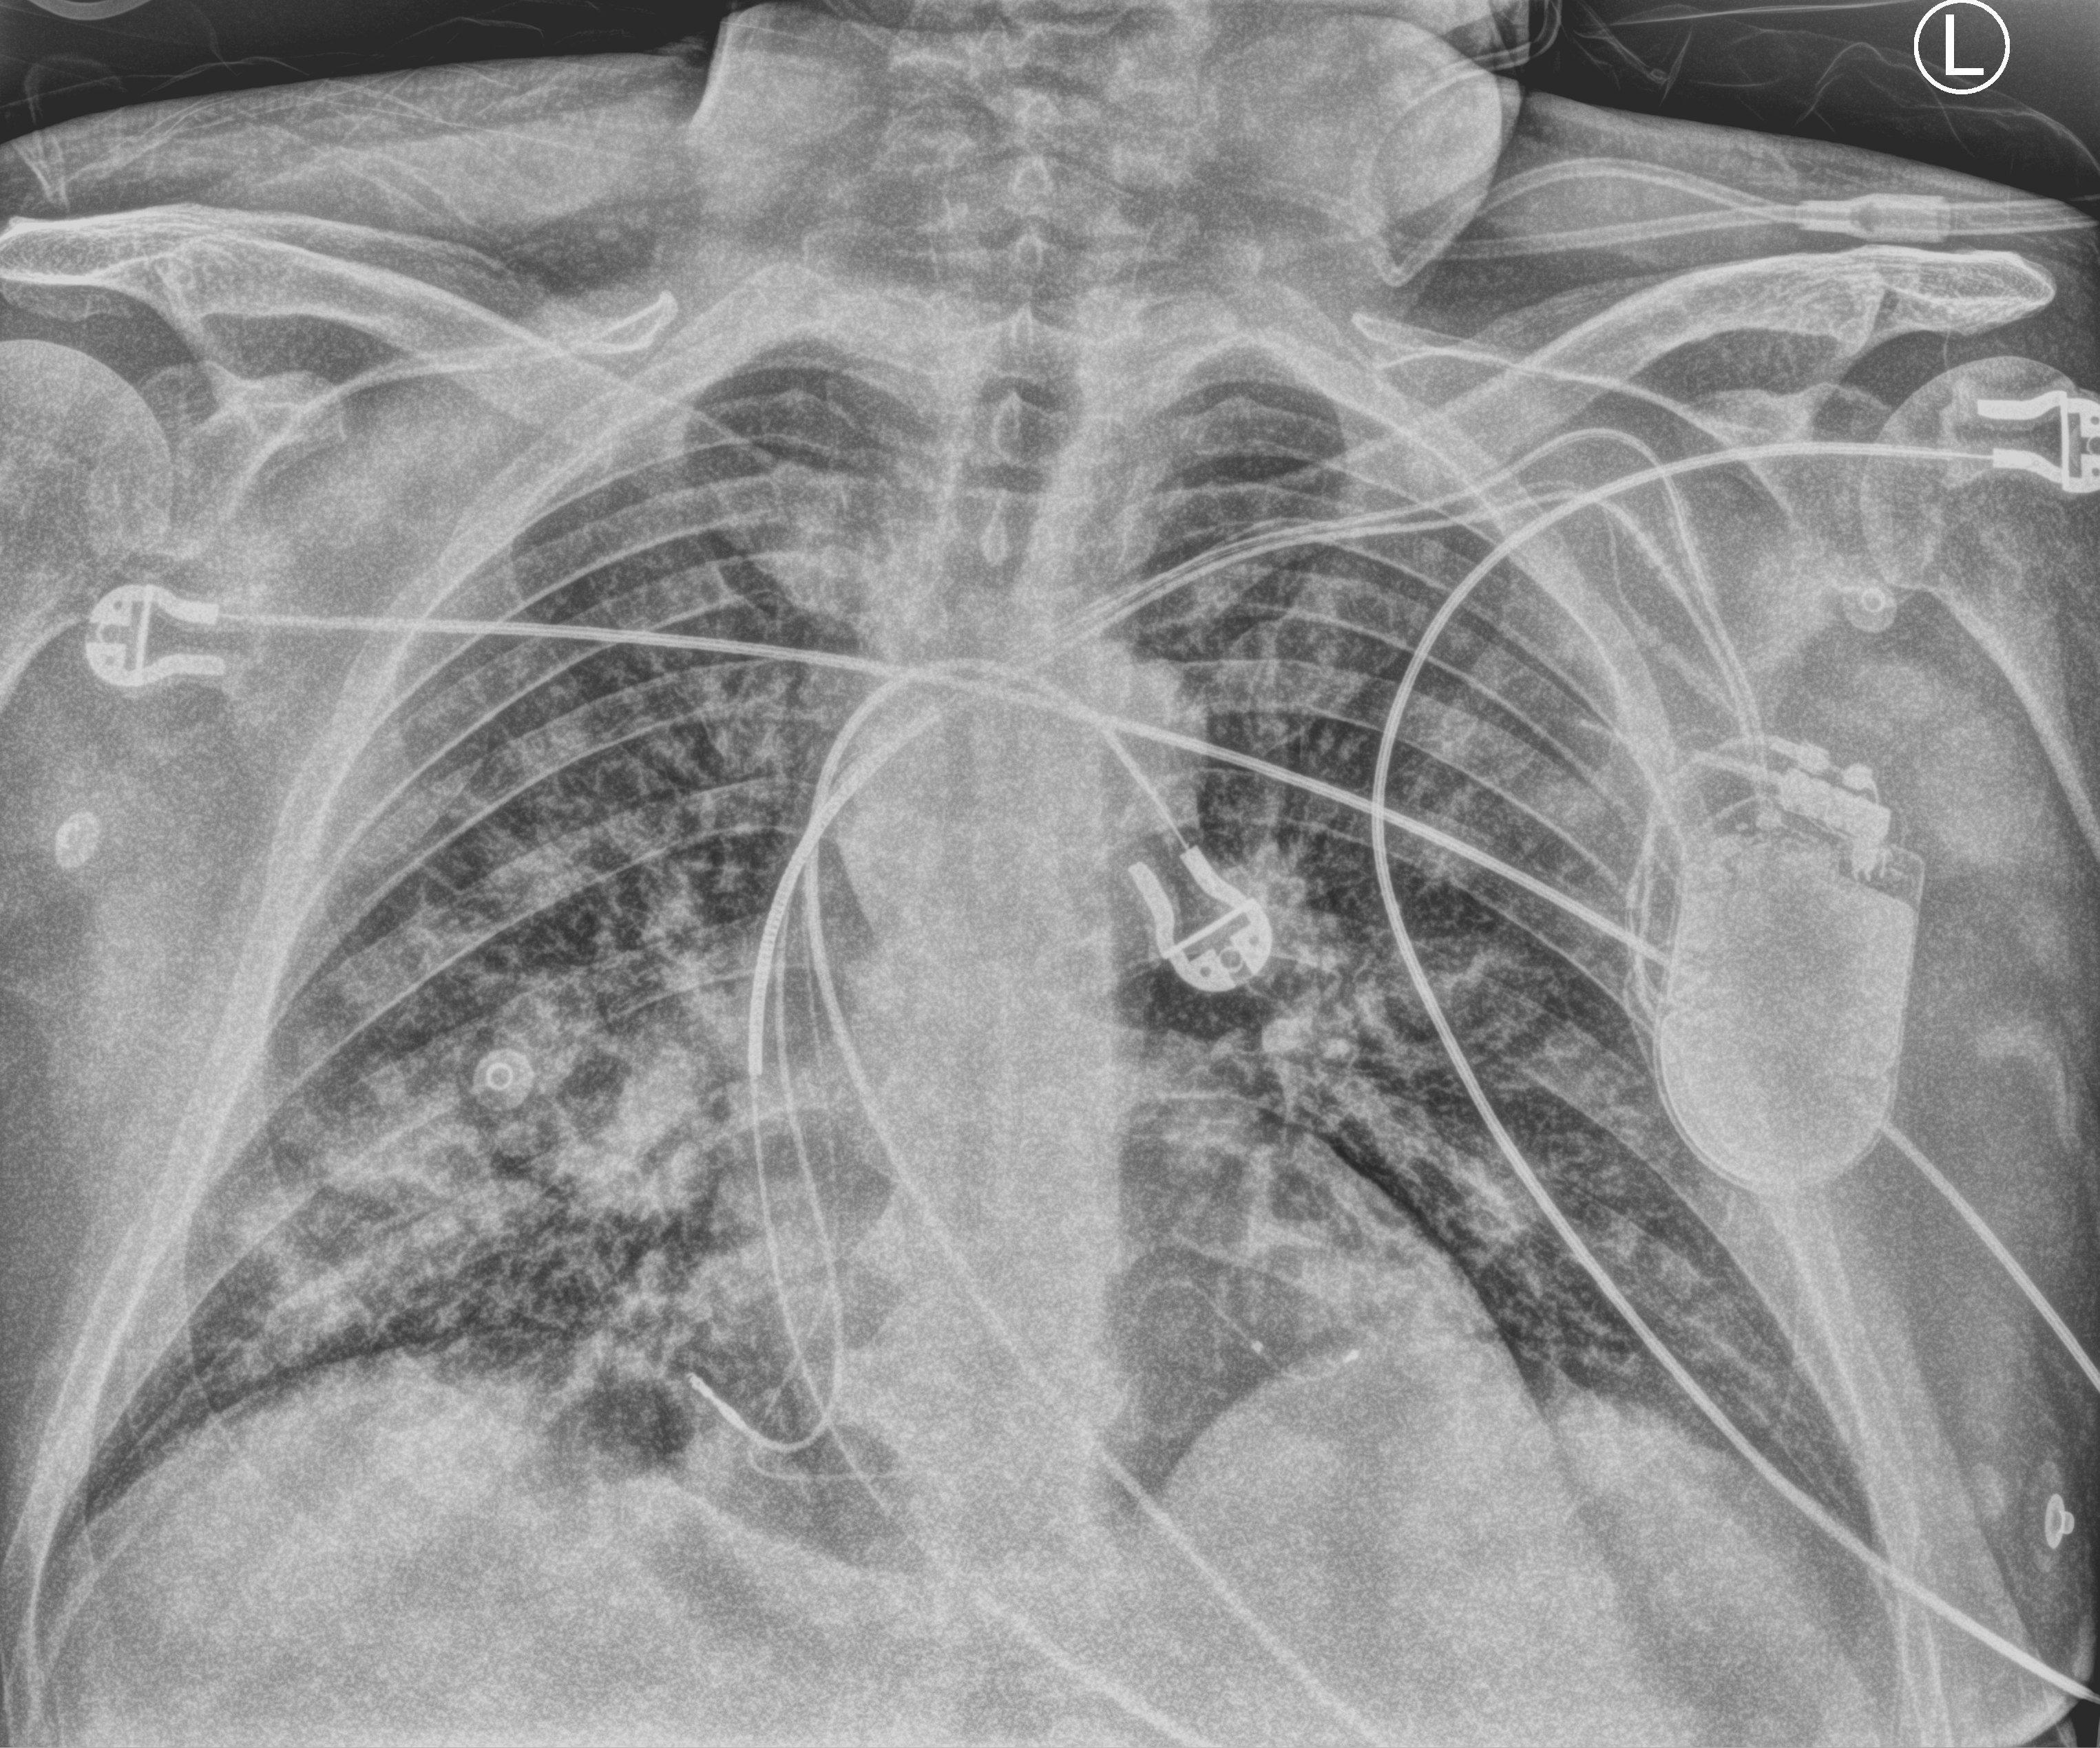
Chest X-ray (portable); anteroposterior (AP) projection. Male patient hospitalised with COVID-19, age 60–74 years.
Admission-level facts for this patient (not findings on this image; timing relative to this image not recorded): other chronic lung disease (admission record): no; mechanically ventilated during this hospital stay: no; admitted to intensive care during this hospital stay: no.